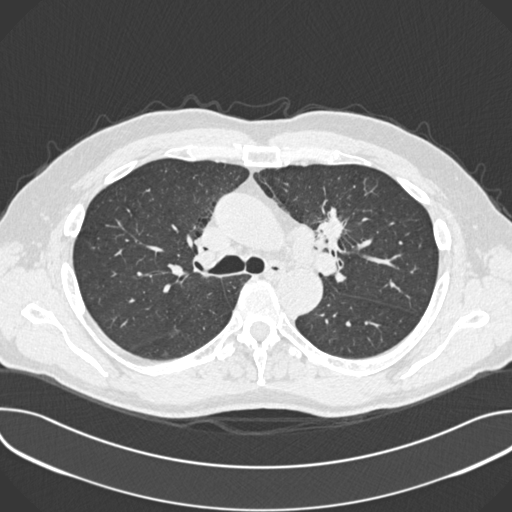
Low-dose screening chest CT, one axial slice. Slice 251 of 361 in the series (ordered by position). Reconstruction kernel B30f. 120 kVp. Lung window (W 1500 / L -600 HU). 1 mm slice thickness. 512 × 512 image matrix, field of view 380 × 380 mm.
Structures marked on this image (expert manual segmentation):
- lesion 1 (tumor, upper lobe of left lung): box from (x=315, y=209) to (x=345, y=248) px